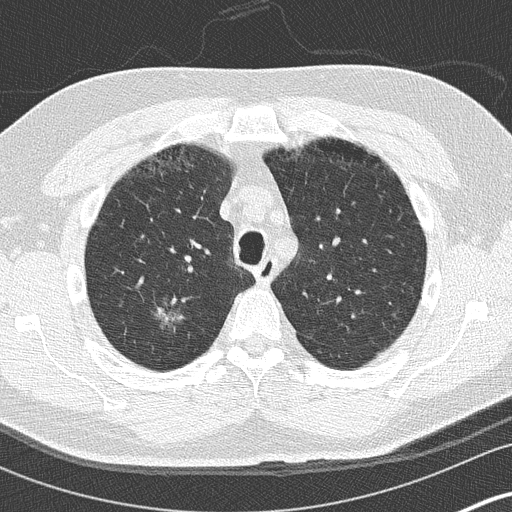
Chest CT (low-dose screening protocol), one axial image; baseline annual screen; lung window (W 1500 / L -600 HU); 2 mm slice thickness; 120 kVp; 512 × 512 image matrix. Male, age 59 years at enrolment.
Lesion marked by an expert reader, bounding box <145,290,199,343> (left, top, right, bottom; pixels). Reader record for this screening exam (exam-level; its link to the box is not recorded): non-calcified nodule or mass ≥4 mm, right upper lobe, 16 × 16 mm, ground glass attenuation. Lung cancer was diagnosed 456 days after this screen (after the second annual screen): bronchiolo-alveolar adenocarcinoma, NOS, right lower lobe, stage IA (AJCC 6th edition), 15 mm at pathology.